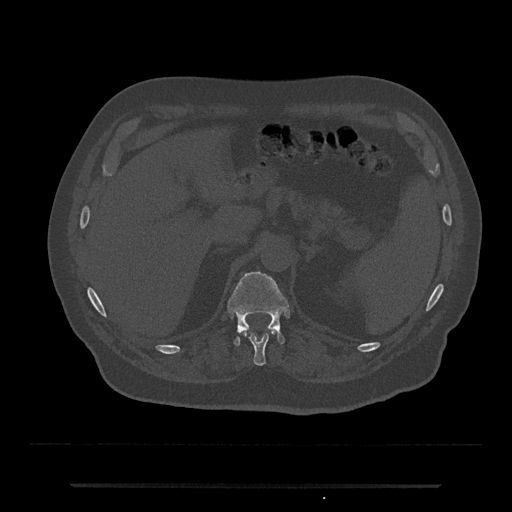
CT including the spine, one axial slice. Position 616 of 797 along the scan axis. Reconstruction kernel Br40s/3. Bone window (W 1800 / L 400 HU). 512 × 512 image matrix, field of view 434 × 434 mm. Male patient, age 80 years. From the clinical record (not read from this slice): primary cancer: prostate.
Structures marked on this image (semi-automatic segmentation, software-assisted and operator-edited):
- T11 vertebra: bounding box [x1, y1, x2, y2] px = [249, 330, 275, 366]
- T12 vertebra: [228, 271, 289, 346]